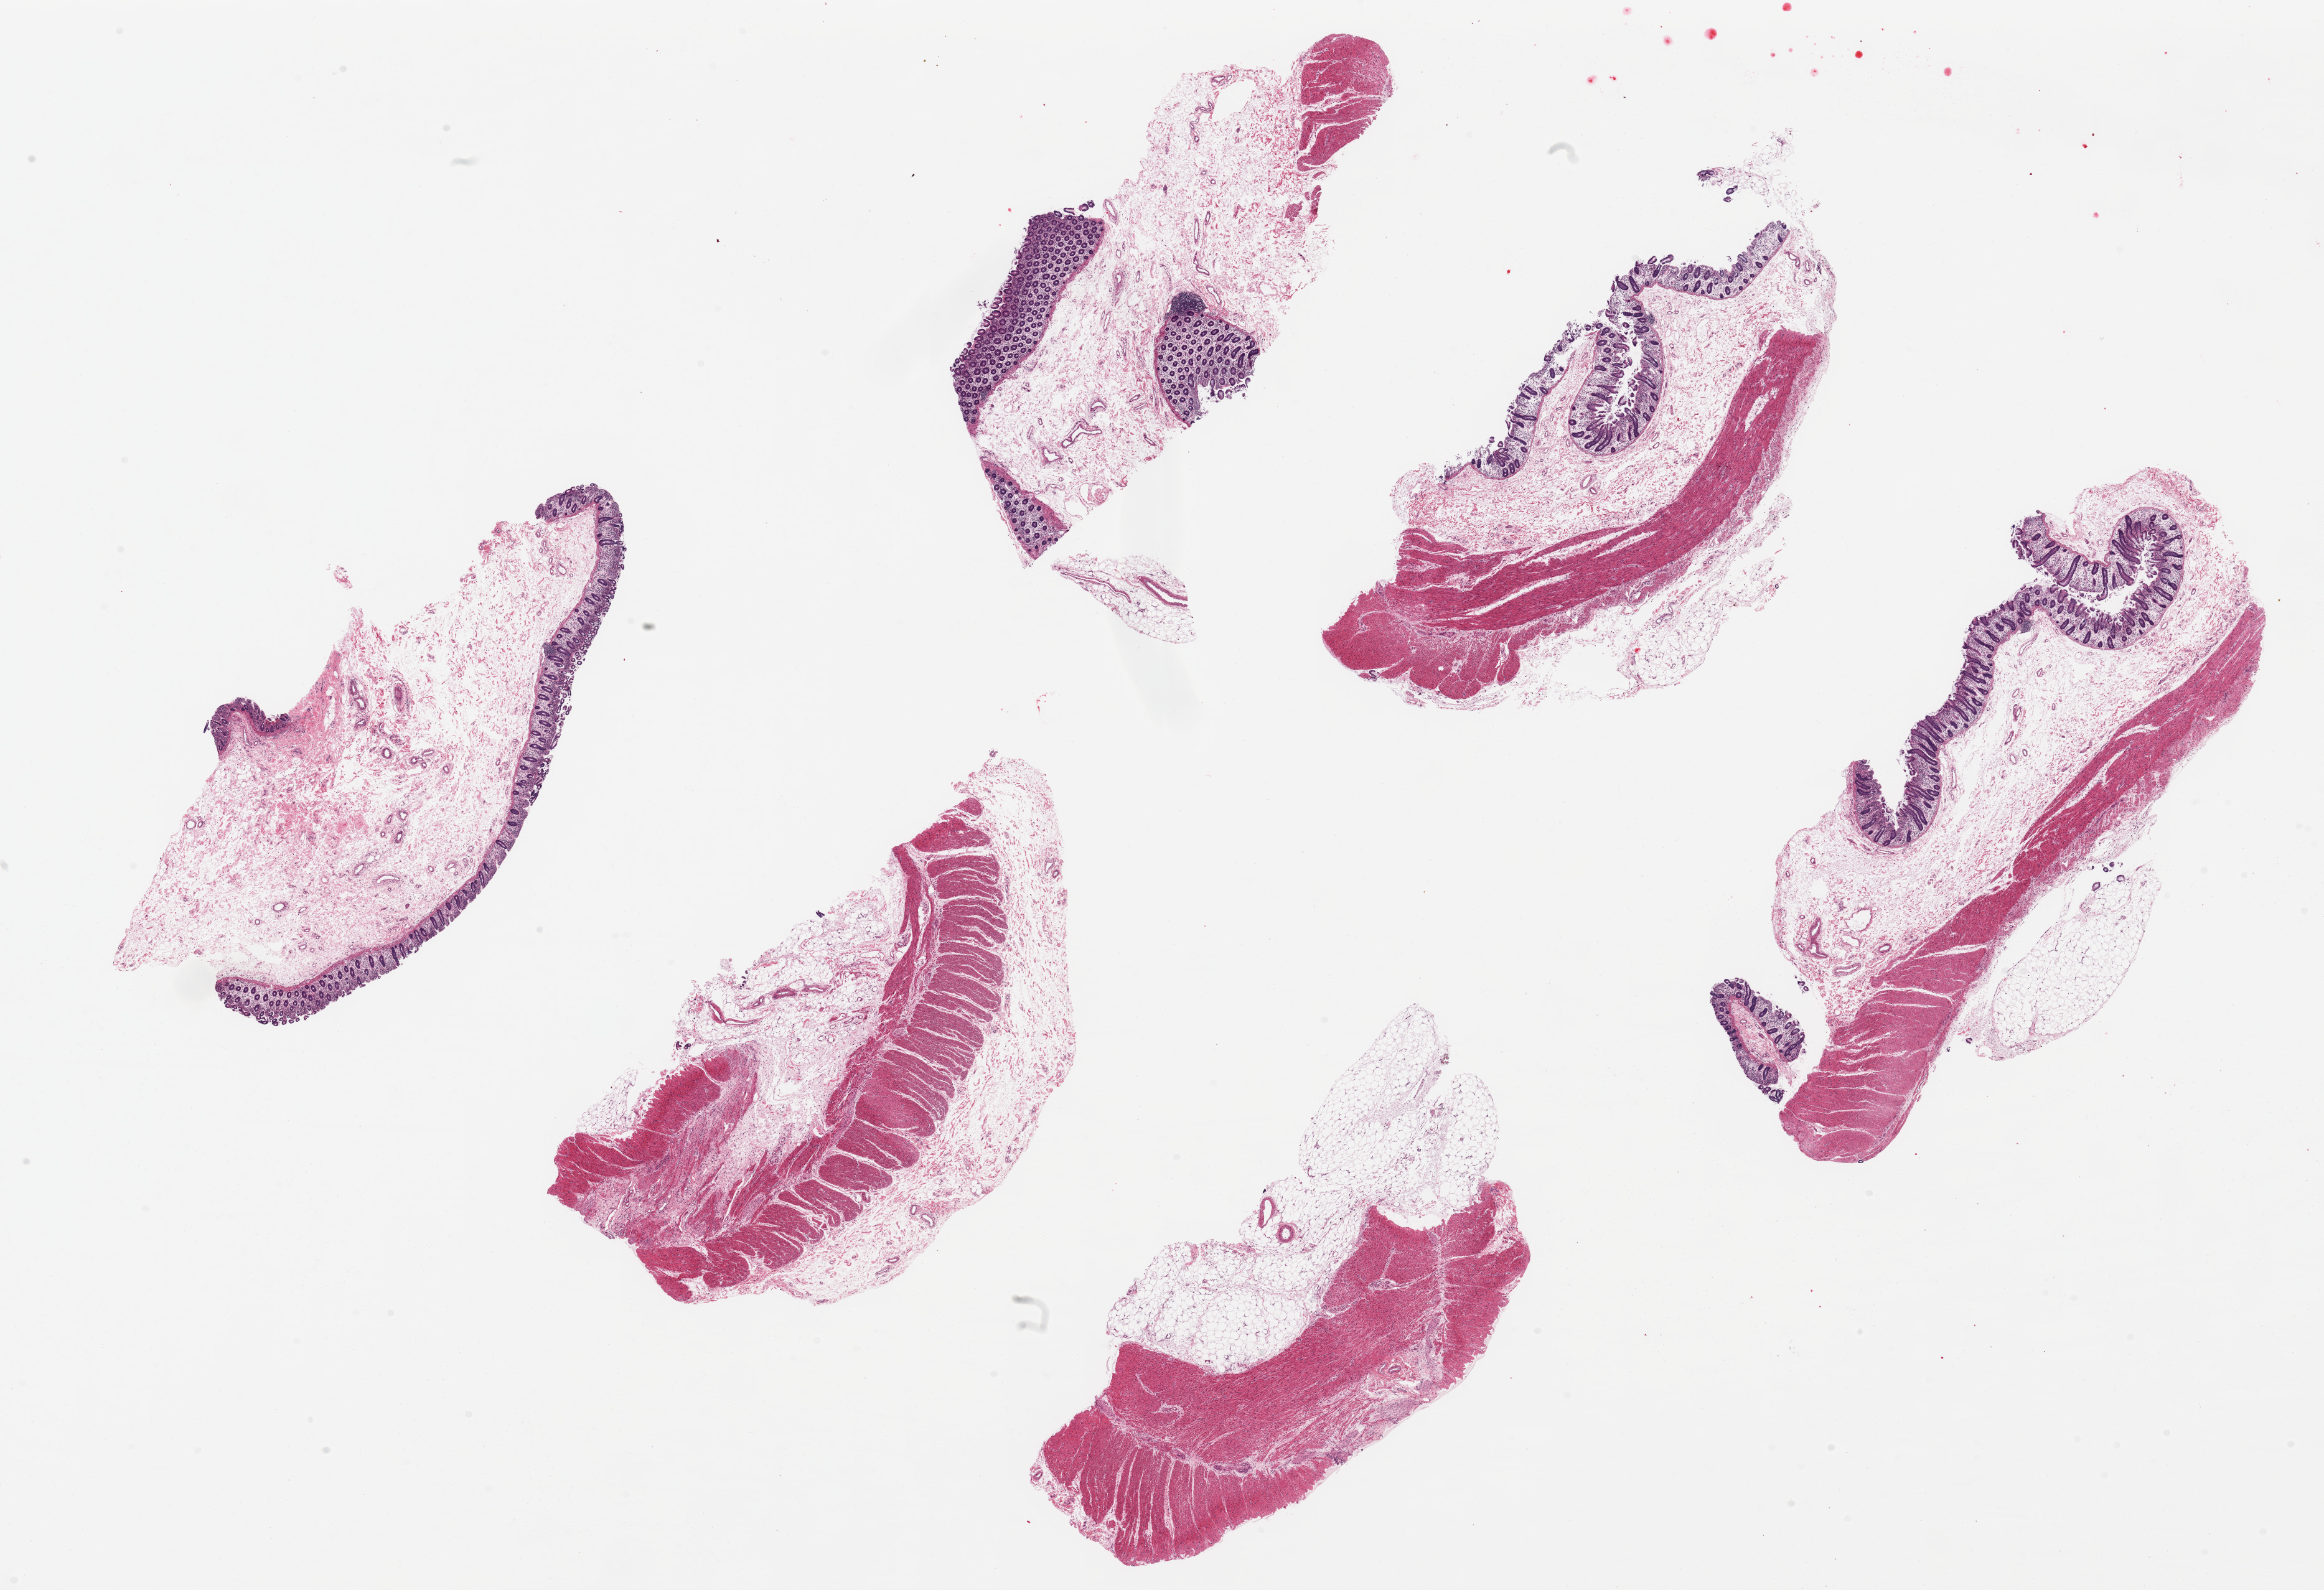
H&E whole-slide image, brightfield, low-resolution overview of the scanned area, about 29.5 x 20.2 mm; PAXgene-fixed paraffin-embedded (PFPE) section; sampled site (target tissue): transverse colon; donor tissue sample. Donor: male.
Pathologist's review note for this sample: 6 ~9x3.5mm pieces; mucosa is ~10-12% thickness, only seen in 4 of 6 pieces.